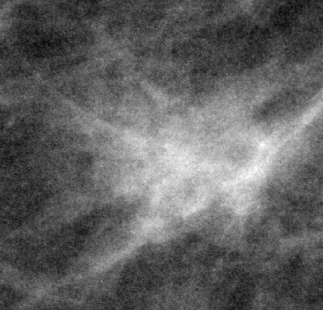
Region of interest cut from a scanned film mammogram (one marked finding); right breast; MLO view.
- Finding: mass, shape irregular, margins microlobulated; BI-RADS assessment category 5; pathology result (as recorded, not read from the image): malignant.